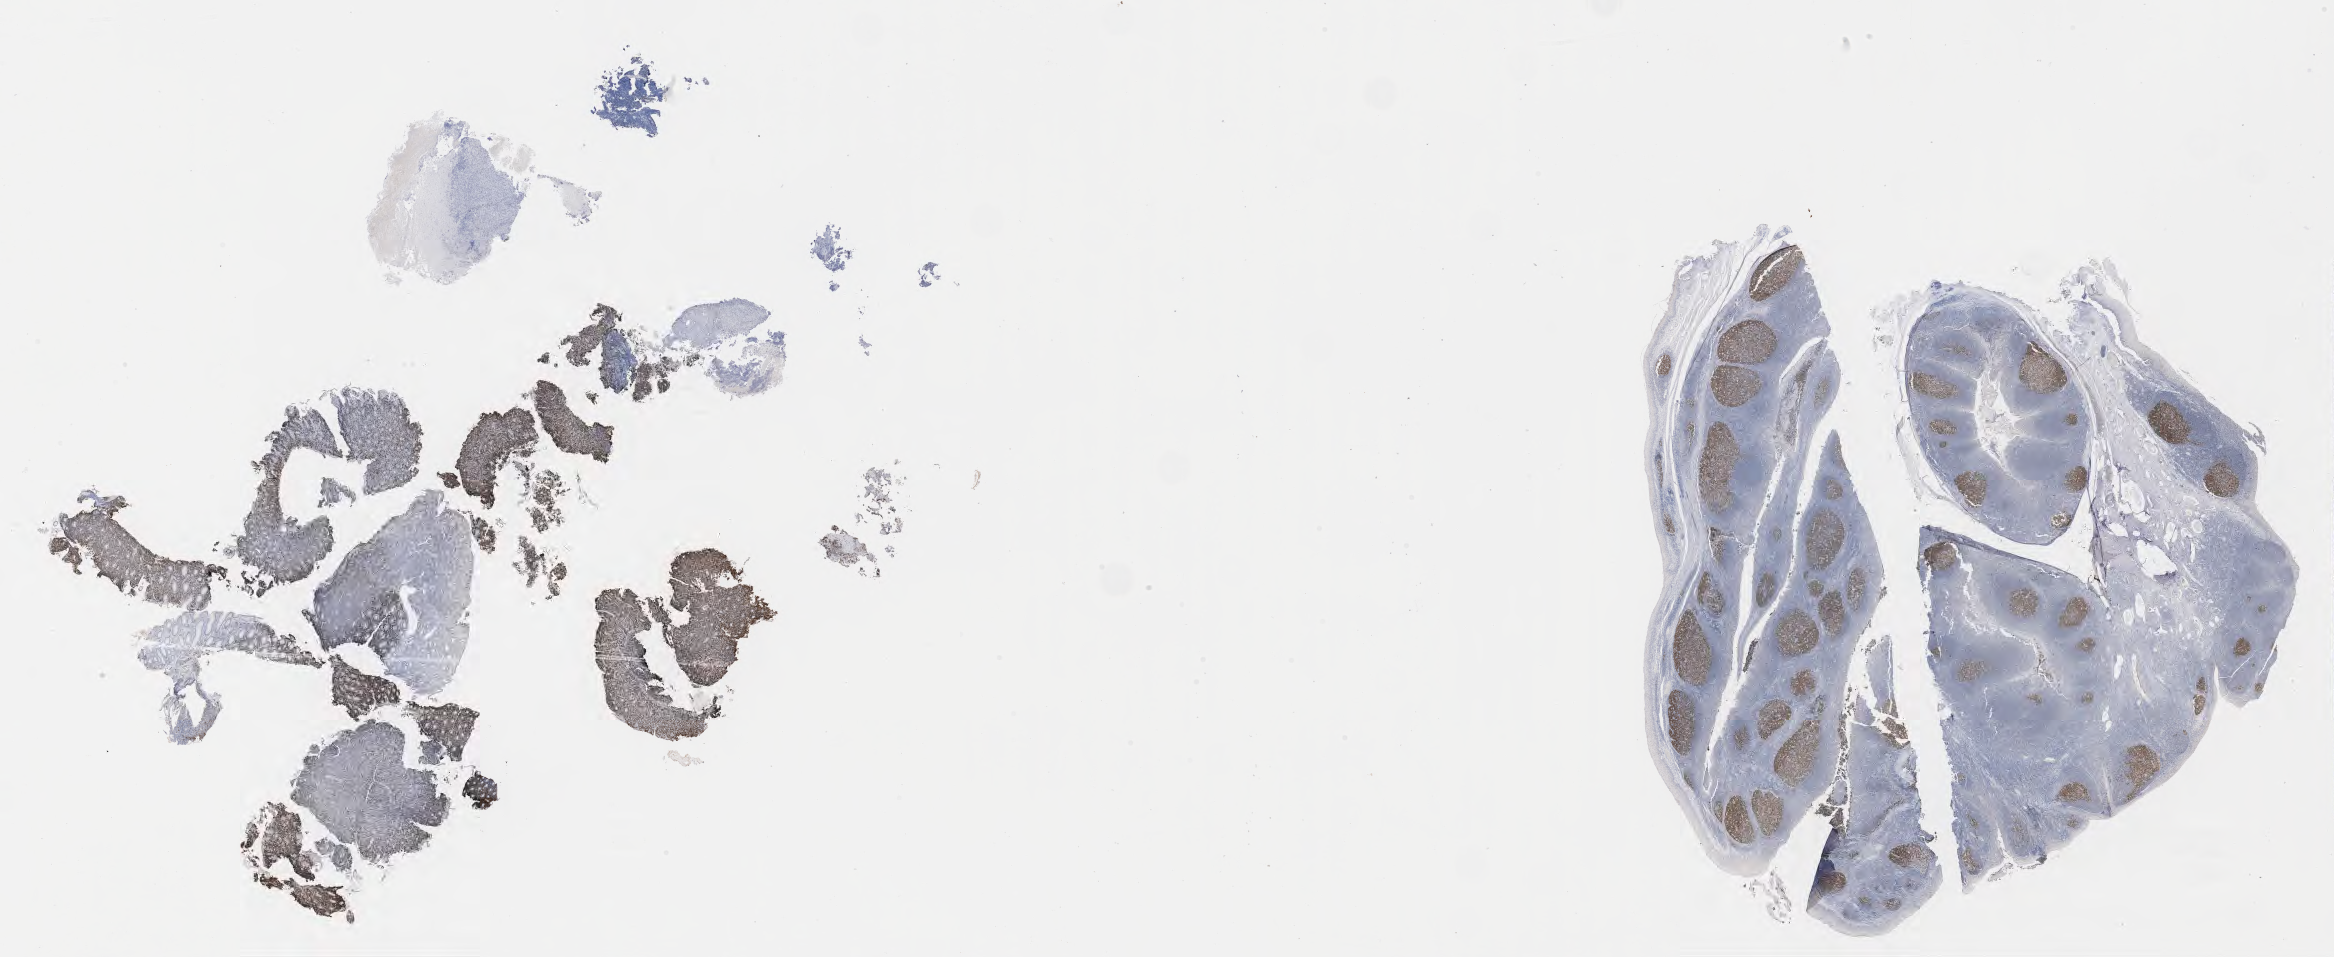
Immunohistochemistry (IHC) whole-slide image stained for BCL6, a low-resolution overview of the entire scanned area, about 37.7 x 15.5 mm. Tumor tissue. Male patient, aged 56.
Histologic diagnosis: Burkitt lymphoma, NOS.